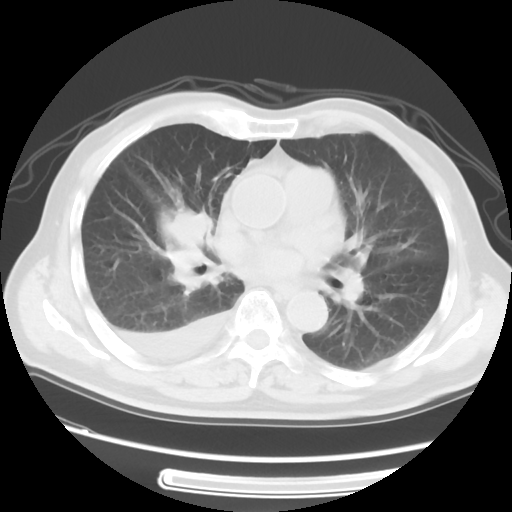
Chest CT, one axial slice. Position 28 of 56 along the scan axis. Reconstruction kernel STANDARD. 120 kVp. Lung window (W 1500 / L -600 HU). 5 mm slice thickness. 512 × 512 image matrix, field of view 360 × 360 mm. Patient: male, 77 years. Case-level facts recorded for this patient, not image findings: clinical TNM (as recorded): T3 N3 M1b.
Structures marked on this image (rectangle marked by the reading radiologist):
- lung tumour (recorded histology: small cell carcinoma): bounding box <150,211,228,292> (left, top, right, bottom; pixels)